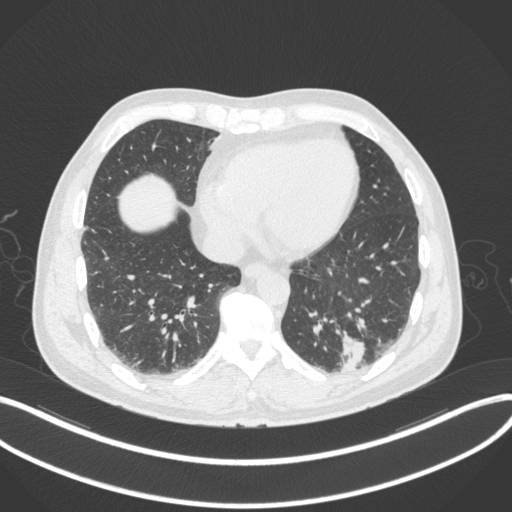
Chest CT, one axial slice. Slice 87 of 313 in the series (ordered by position). Reconstruction kernel B31f. Lung window (W 1500 / L -600 HU). 1 mm slice thickness. 512 × 512 image matrix. Patient: male, 54 years. From the clinical record (not read from this slice): clinical TNM (as recorded): T1c N0 M1; histopathological grade: G3.
Outlined on this slice (rectangle marked by the reading radiologist):
- lung tumour (recorded histology: adenocarcinoma): bounding box [x1, y1, x2, y2] px = [333, 329, 369, 376]